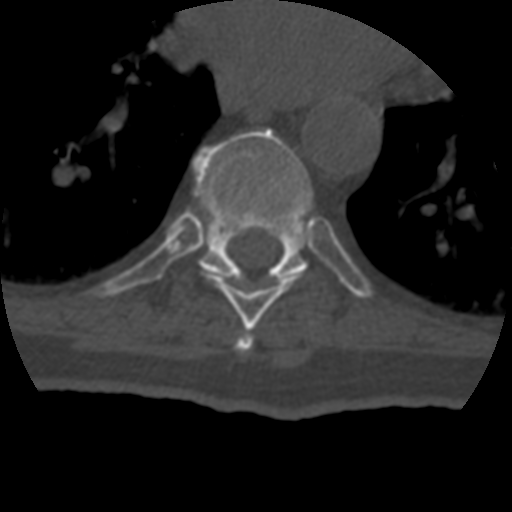
CT including the spine, one axial slice; reconstruction kernel STANDARD; 120 kVp; bone window (W 1800 / L 400 HU); 1.25 mm slice thickness; 512 × 512 image matrix, field of view 160 × 160 mm. Patient age 69 years. Case-level facts recorded for this patient, not image findings: primary cancer: prostate.
Outlined on this slice (semi-automatically segmented with operator editing):
- T7 vertebra: bounding box [x1, y1, x2, y2] px = [235, 332, 254, 352]
- T8 vertebra: [201, 267, 301, 331]
- T9 vertebra: [195, 129, 313, 279]